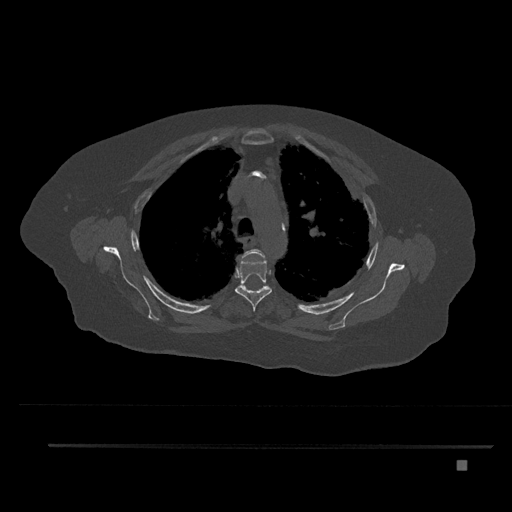
CT including the spine, one axial slice. 120 kVp. Bone window (W 1800 / L 400 HU). 0.5 mm slice thickness. 512 × 512 image matrix, field of view 437 × 437 mm. Patient: female, 76 years. From the clinical record (not read from this slice): primary cancer: lung.
Annotated regions visible in this slice (semi-automatic segmentation, software-assisted and operator-edited):
- T3 vertebra: bounding box <242,249,265,259> (left, top, right, bottom; pixels)
- T4 vertebra: <234,255,272,311>
- T5 vertebra: <245,287,262,291>